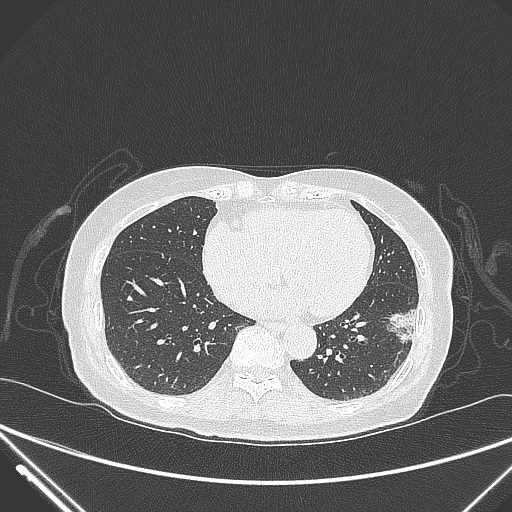
Chest CT, one axial slice. Position 110 of 310 along the scan axis. Lung window (W 1500 / L -600 HU). 1 mm slice thickness. 512 × 512 image matrix, field of view 377 × 377 mm. Female patient, age 82 years. Case-level facts recorded for this patient, not image findings: clinical TNM (as recorded): T1c N0 M0; histopathological grade: G2.
Structures marked on this image (bounding box drawn by a radiologist):
- lung tumour (recorded histology: adenocarcinoma): bounding box (x1, y1, x2, y2) in pixels: (389, 304, 437, 350)